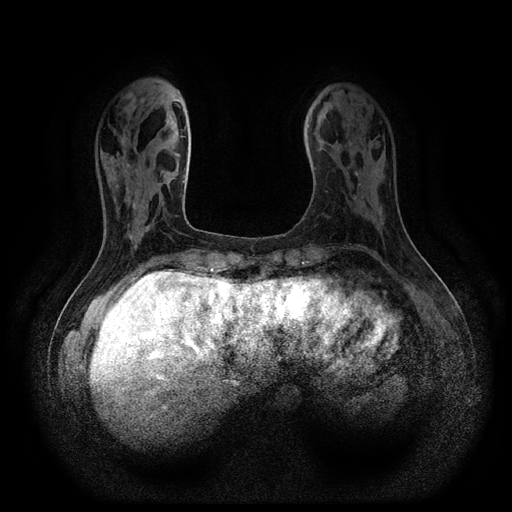
Breast MRI (dynamic contrast-enhanced, multi-phase), one axial slice; position 31 of 116 along the scan axis; dynamic contrast-enhanced series, time point 2 of 5 at this slice position (early post-contrast); 1.5 T; TE 2.6 ms, TR 5.3 ms; 2.2 mm slice thickness; 512 × 512 image matrix, field of view 340 × 340 mm. Patient: female, 54 years.
Structures marked on this image (semi-automatic segmentation, software-assisted and operator-edited):
- breast lesion (labelled benign in the annotation): box from (x=353, y=195) to (x=358, y=201) px